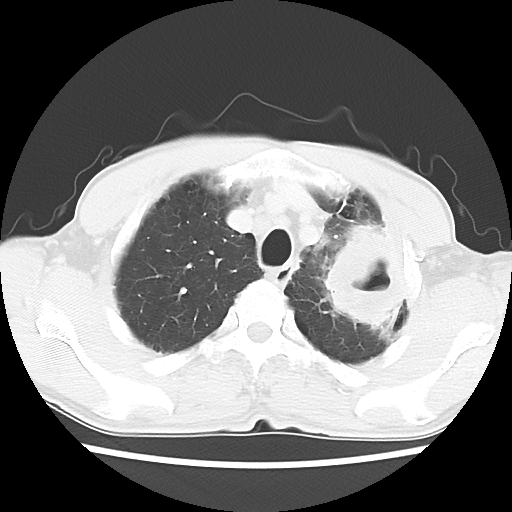
Chest CT, one axial slice; position 49 of 60 along the scan axis; reconstruction kernel LUNG; 120 kVp; lung window (W 1500 / L -600 HU); 5 mm slice thickness; 512 × 512 image matrix, field of view 308 × 308 mm. Male patient, age 64 years. From the clinical record (not read from this slice): clinical TNM (as recorded): T3 N3 M0; histopathological grade: G3.
Outlined on this slice (rectangle marked by the reading radiologist):
- lung tumour (recorded histology: adenocarcinoma): box from (x=315, y=218) to (x=416, y=339) px